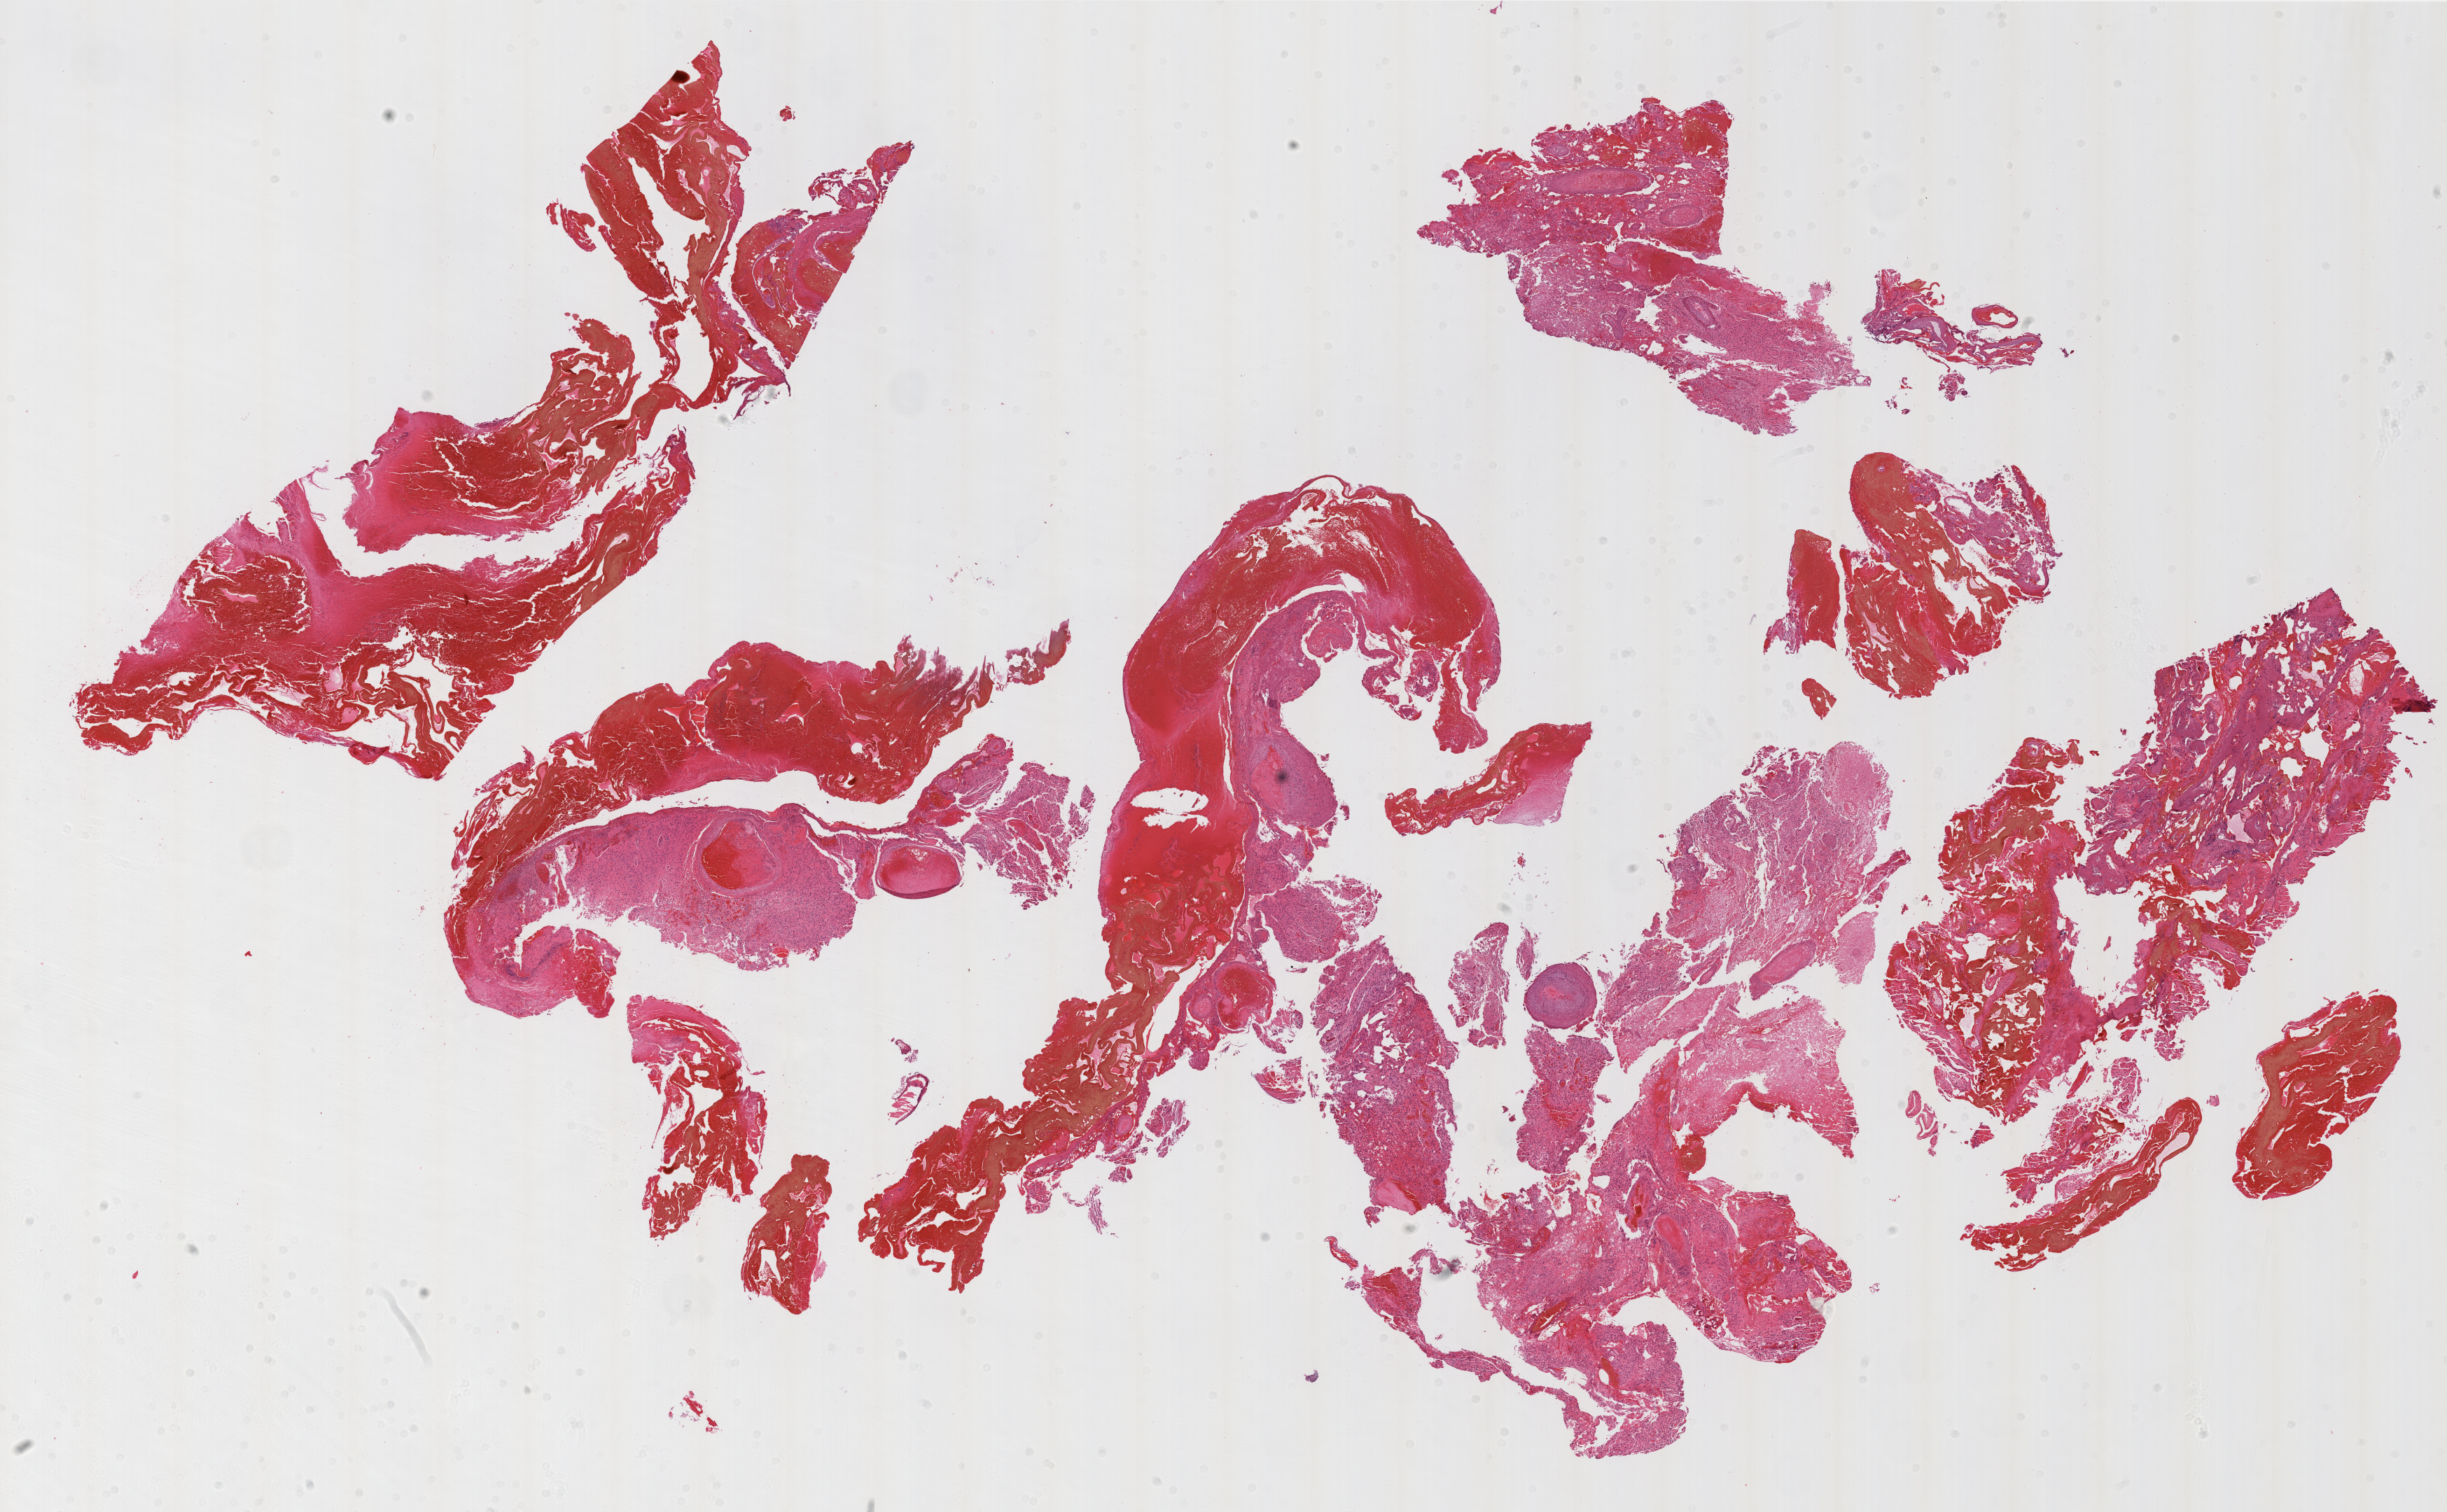
Whole-slide histology image, H&E-stained, shown as a low-resolution overview of the whole scanned area (about 28.0 x 17.3 mm, acquisition: 20x scan); FFPE section; sample: primary tumour, brain. Male patient; age at initial diagnosis 76 years.
Pathologic diagnosis: Glioblastoma.